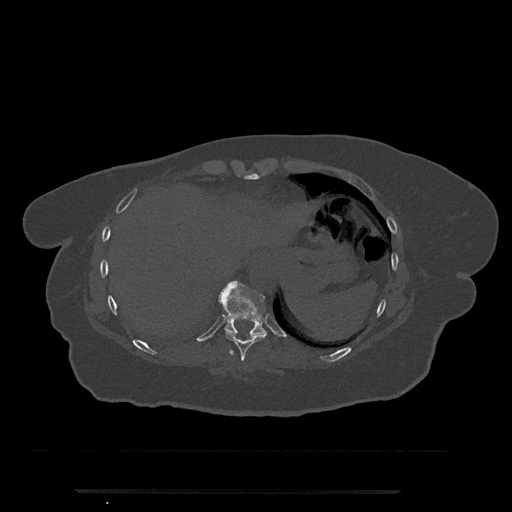
CT including the spine, one axial slice; slice 315 of 797 in the series (ordered by position); reconstruction kernel Br40s/3; 120 kVp; bone window (W 1800 / L 400 HU); 0.5 mm slice thickness; 512 × 512 image matrix, field of view 440 × 440 mm. Patient: female, 51 years. Case-level facts recorded for this patient, not image findings: primary cancer: neuro; vertebrae with lytic lesions (as recorded): T8.
Structures marked on this image (semi-automatically segmented with operator editing):
- T10 vertebra: bounding box <218,281,267,337> (left, top, right, bottom; pixels)
- T9 vertebra: <226,332,267,361>